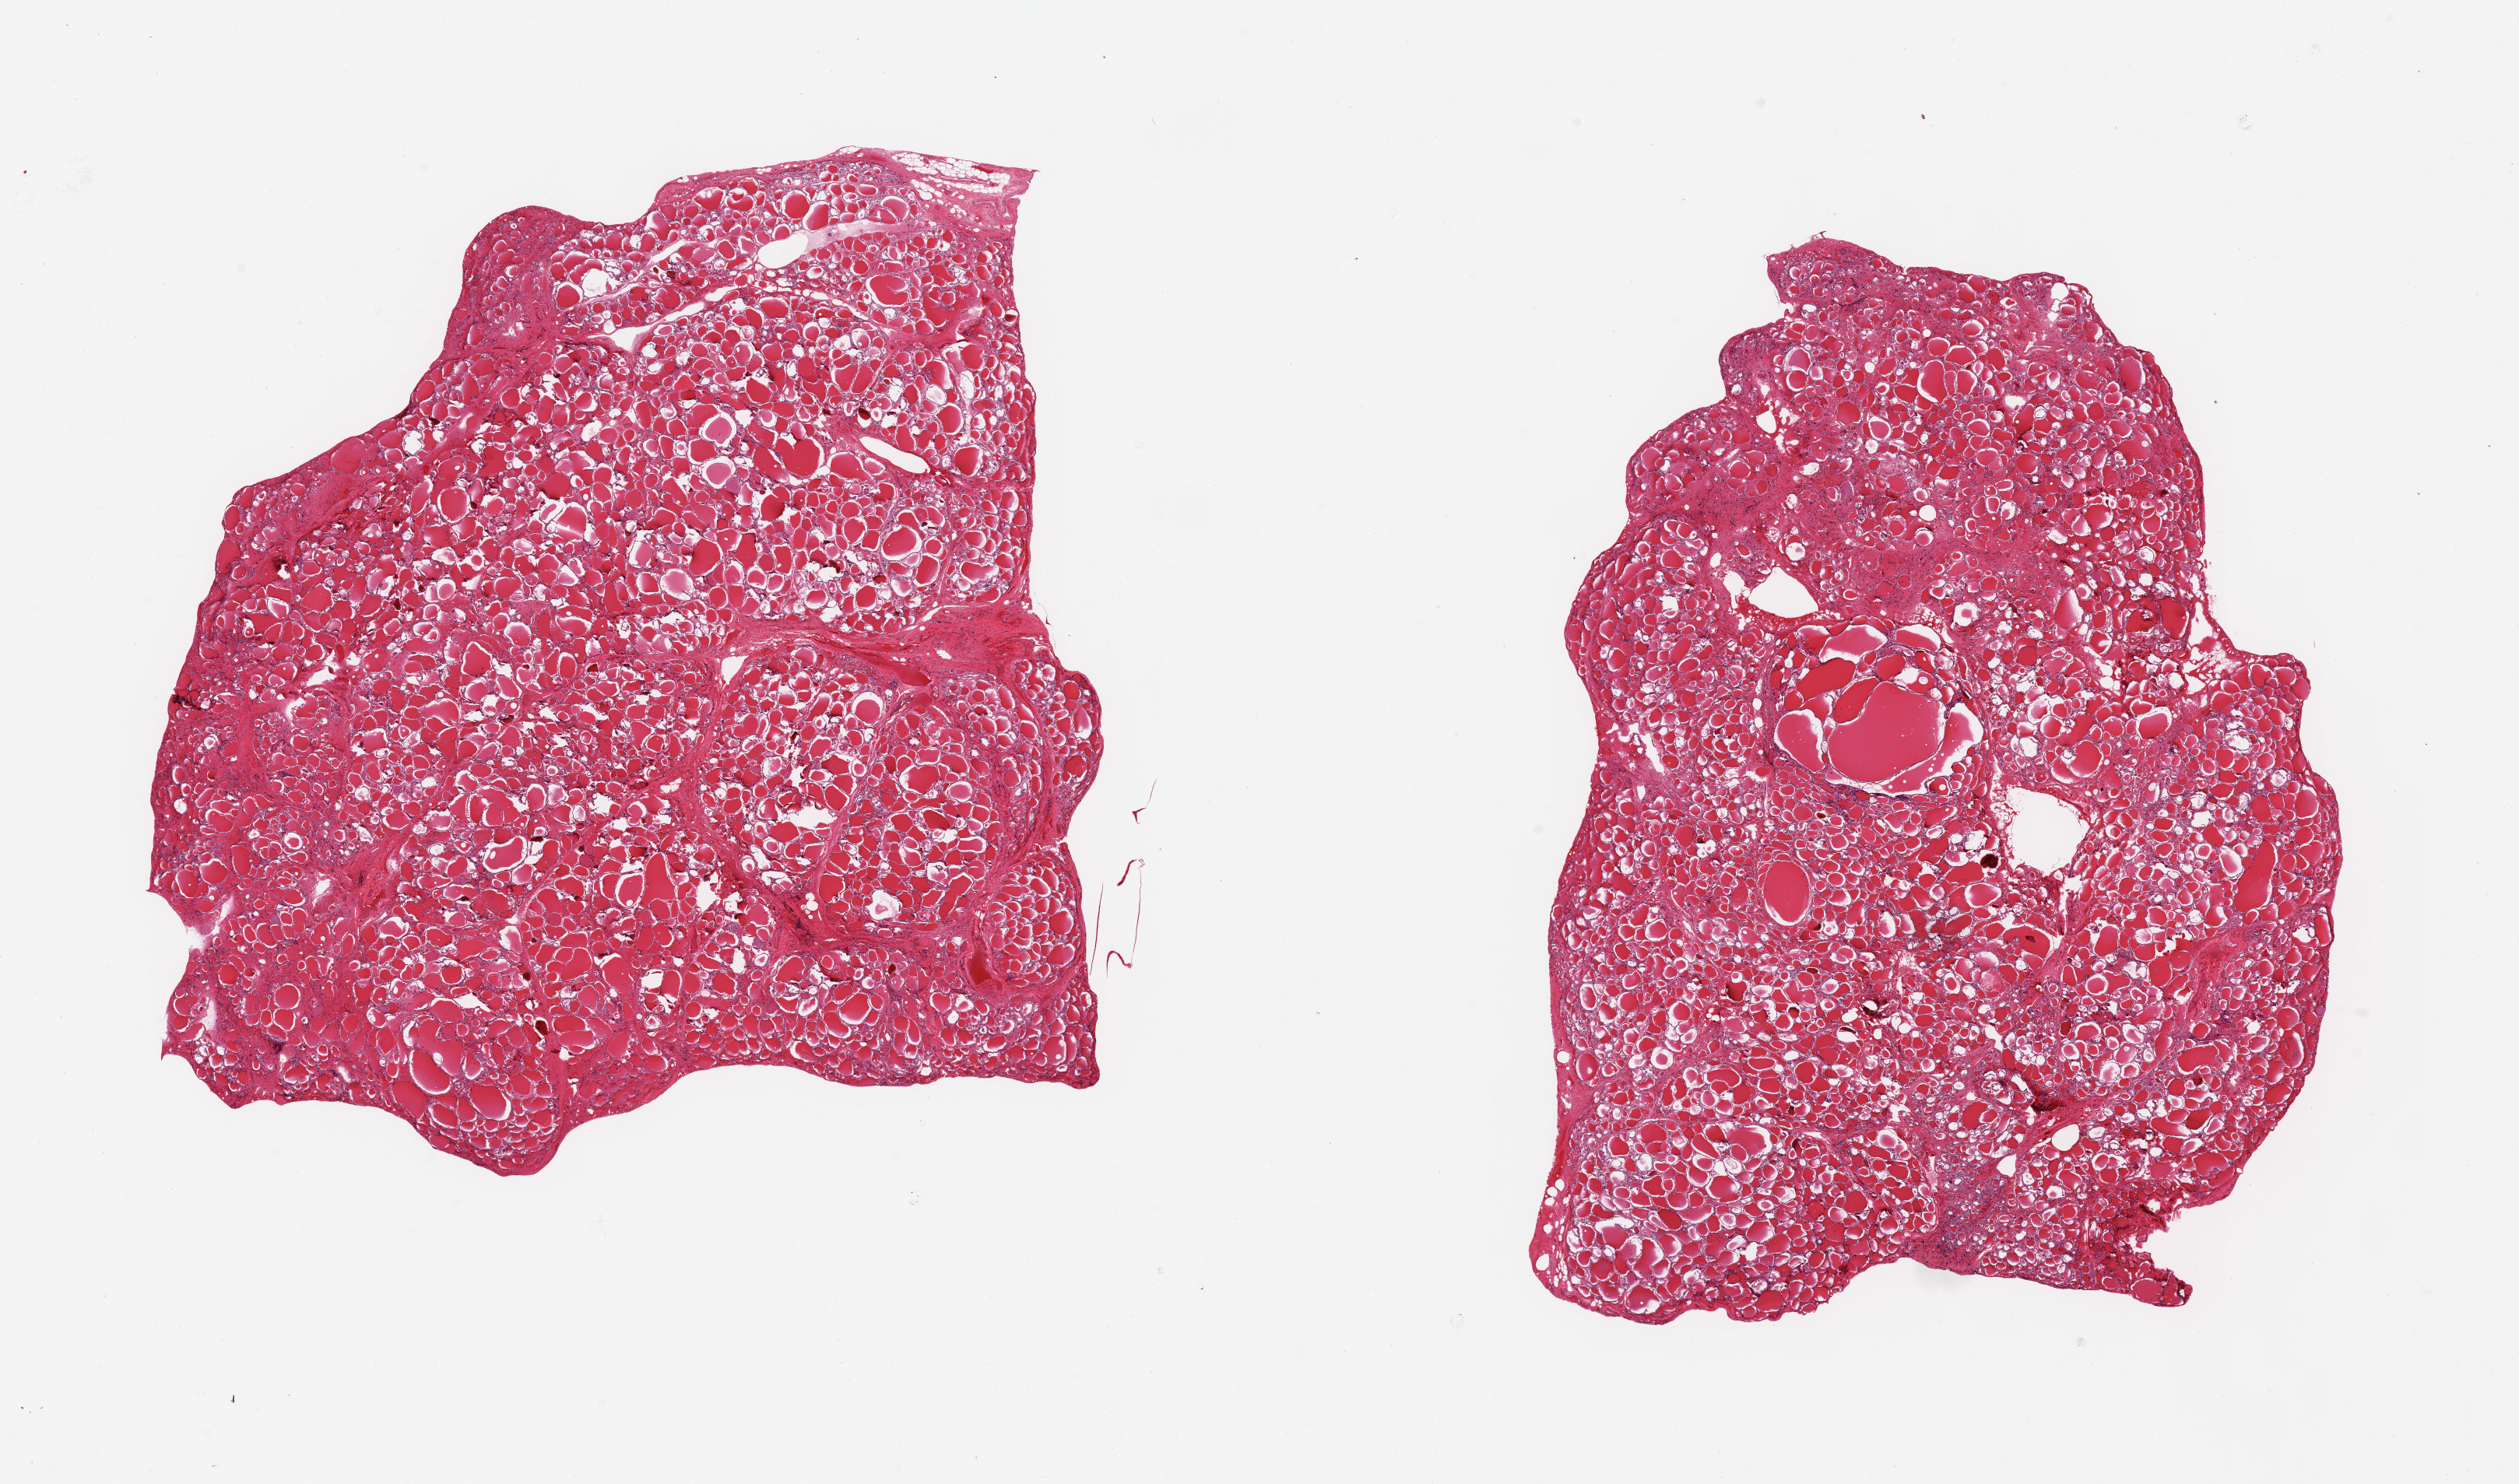
Digitized H&E-stained section, brightfield — a low-resolution overview of the entire scanned area, about 25.6 x 15.1 mm, PAXgene-fixed, paraffin-embedded tissue, section of thyroid (target tissue), donor tissue sample. Male donor.
Reviewer comment on this tissue sample: 2 pieces, a few minute colloid cysts (~1.5mm).